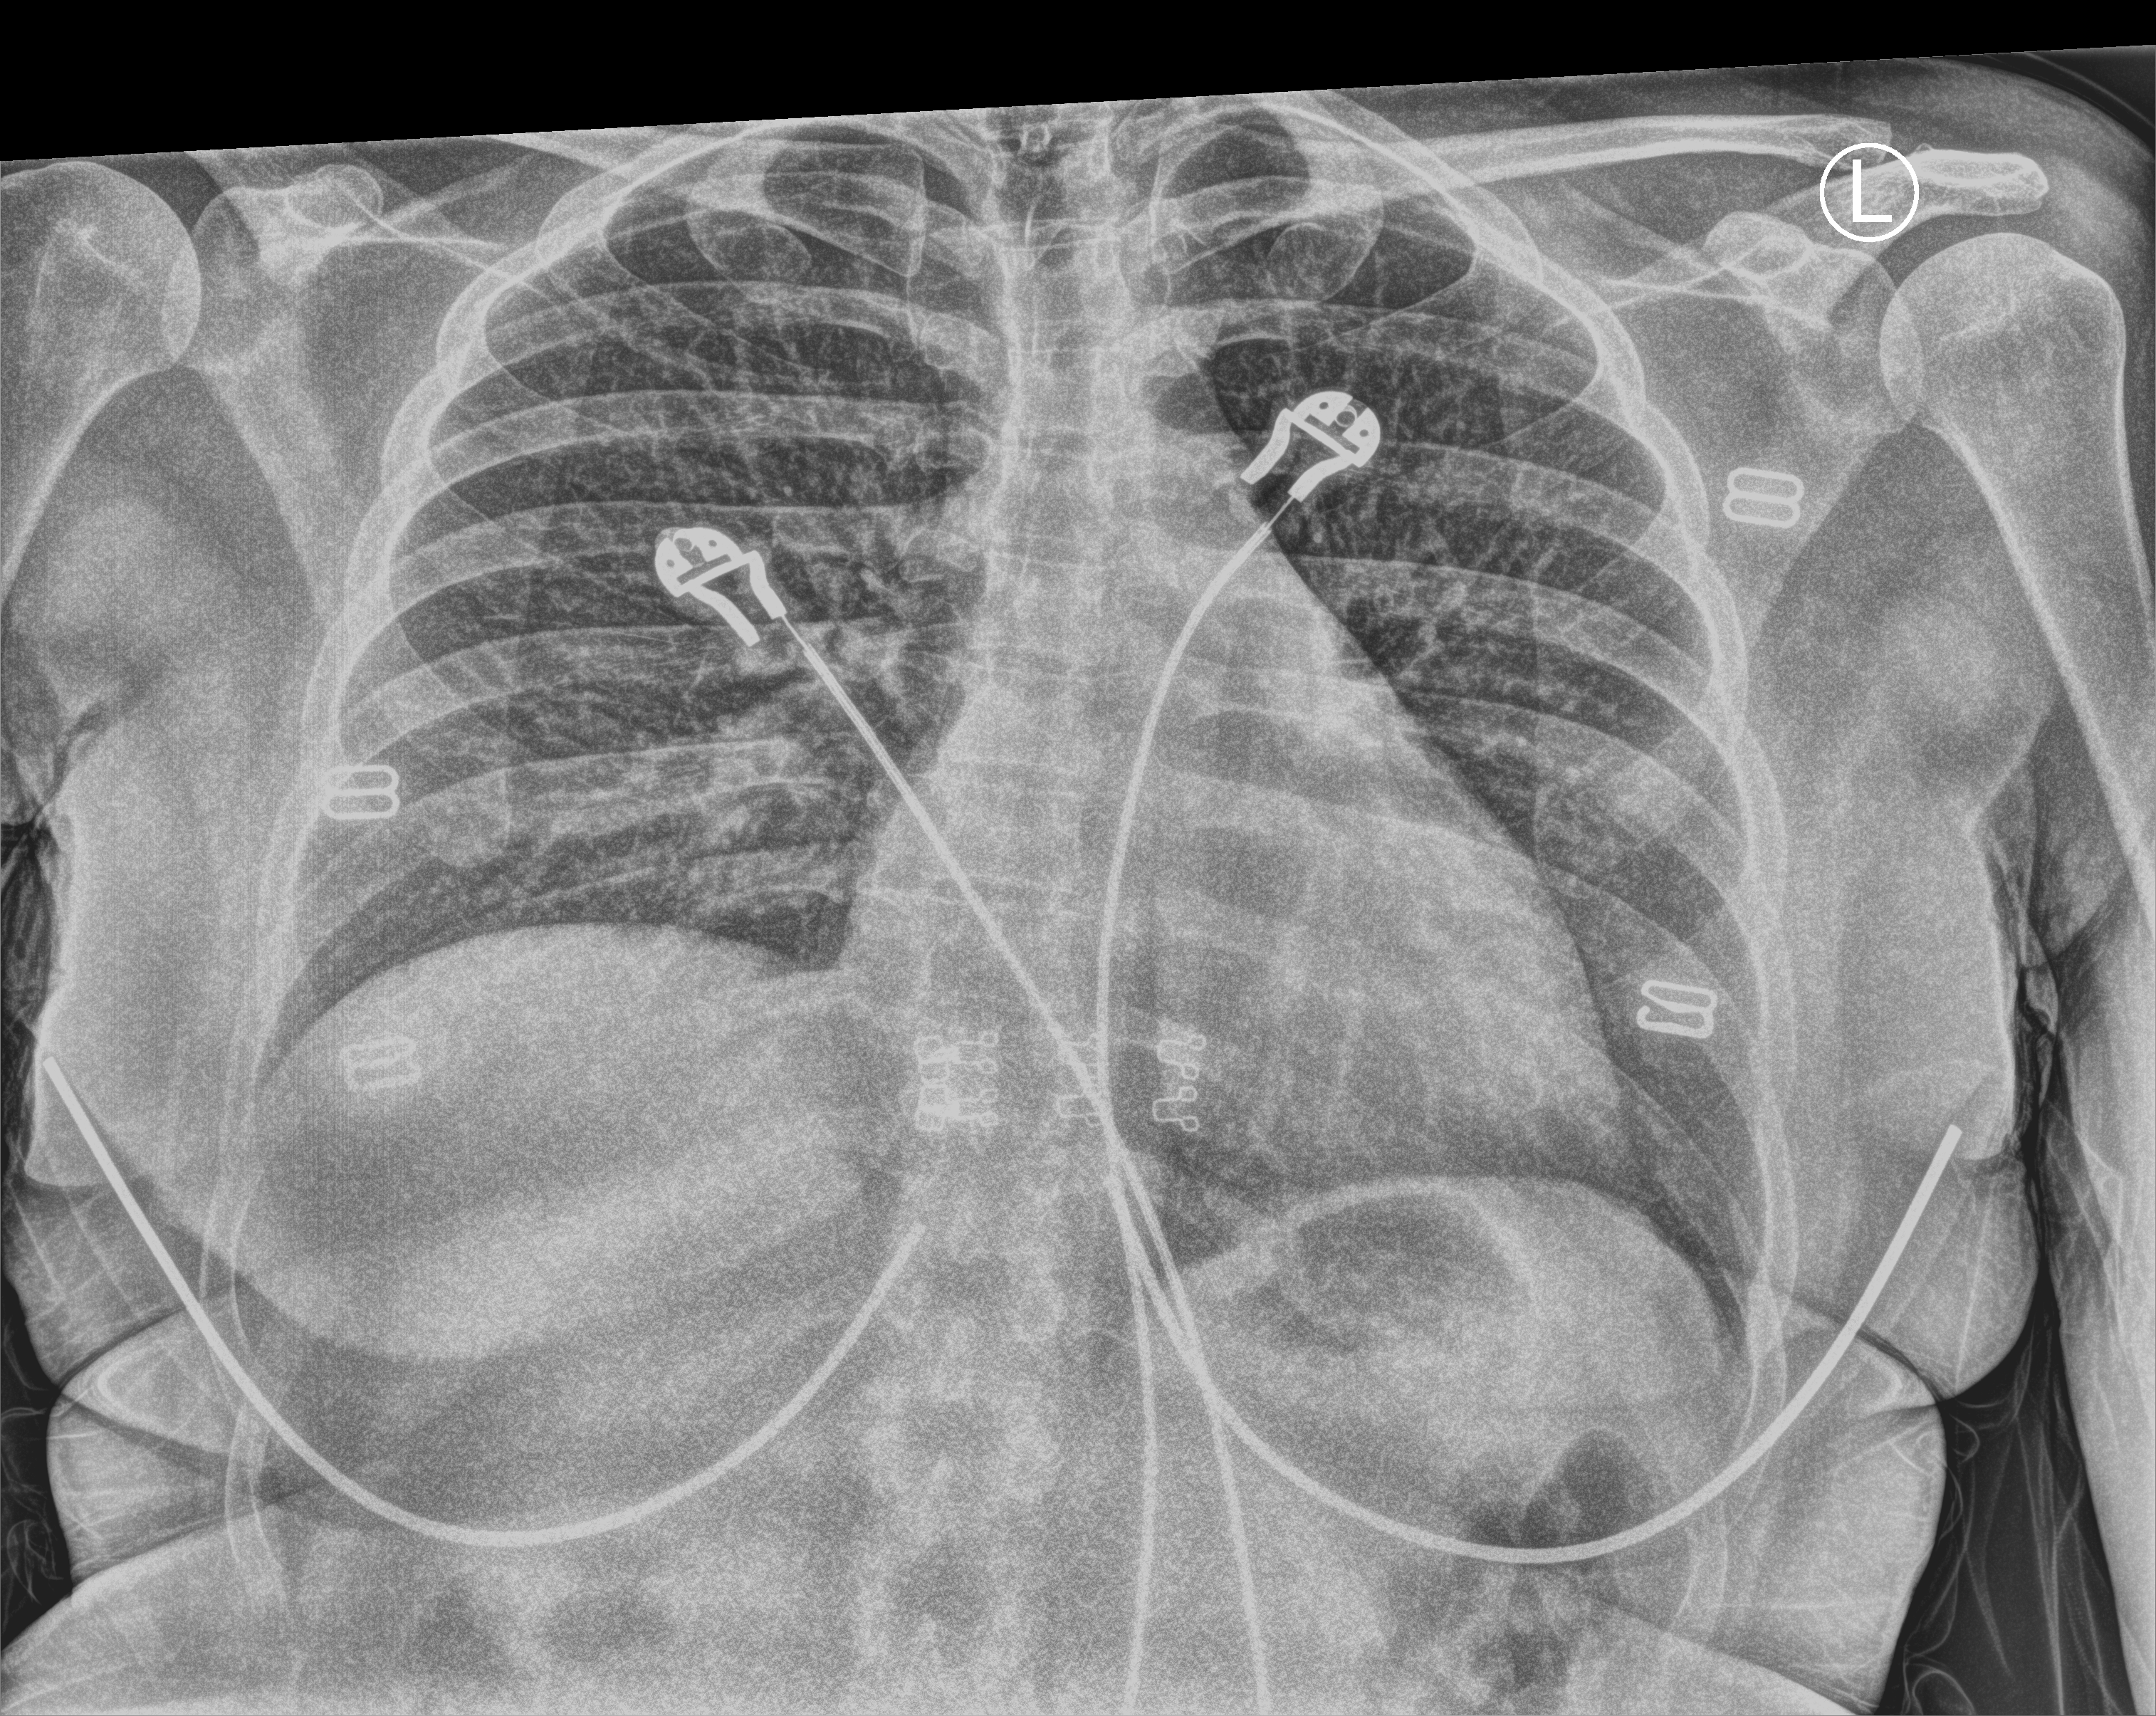
Portable chest radiograph; anteroposterior (AP) projection. Female patient hospitalised with COVID-19, age 18–59 years.
Hospital-stay facts (about this admission, not read from this image; timing relative to this image not recorded):
- admitted to intensive care during this hospital stay: no
- mechanically ventilated during this hospital stay: no